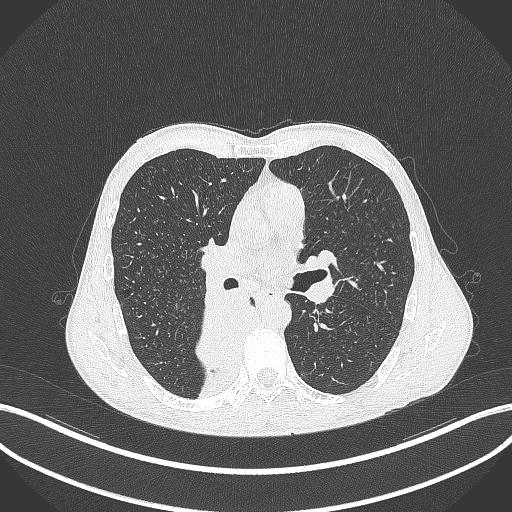
Chest CT, one axial slice; position 213 of 371 along the scan axis; 120 kVp; lung window (W 1500 / L -600 HU); 512 × 512 image matrix, field of view 400 × 400 mm. Male patient, age 58 years. Case-level facts recorded for this patient, not image findings: clinical TNM (as recorded): T3 N1 M1.
Annotated regions visible in this slice (rectangle marked by the reading radiologist):
- lung tumour (recorded histology: squamous cell carcinoma): bounding box <192,291,248,371> (left, top, right, bottom; pixels)